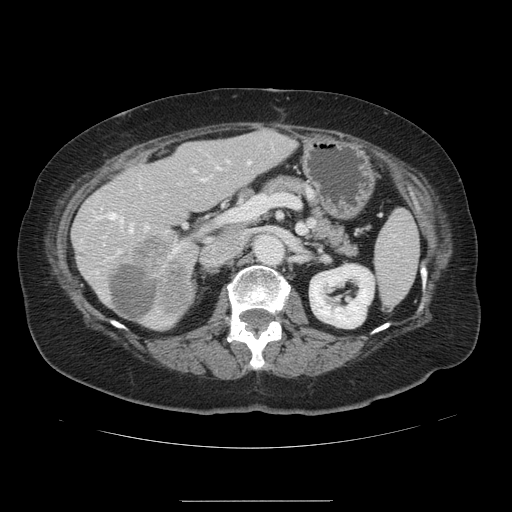
Contrast-enhanced abdominal CT, one axial slice. Slice 64 of 141 in the series (ordered by position). 120 kVp. Intravenous contrast given. Soft-tissue window (W 400 / L 40 HU). 512 × 512 image matrix. Female patient, age 74 years. From the clinical record (not read from this slice): diagnosis: colorectal cancer liver metastases, imaged before liver resection; multiple liver metastases: yes; largest metastasis: 7 cm.
Outlined on this slice (manually delineated by an expert):
- hepatic veins: bounding box (x1, y1, x2, y2) in pixels: (108, 184, 142, 234)
- liver: (73, 130, 294, 329)
- planned liver remnant (the part of the liver to remain after resection): (82, 130, 294, 326)
- portal vein (with intrahepatic branches): (117, 160, 250, 253)
- liver metastasis: (111, 264, 158, 321)
- liver metastasis: (131, 237, 192, 312)